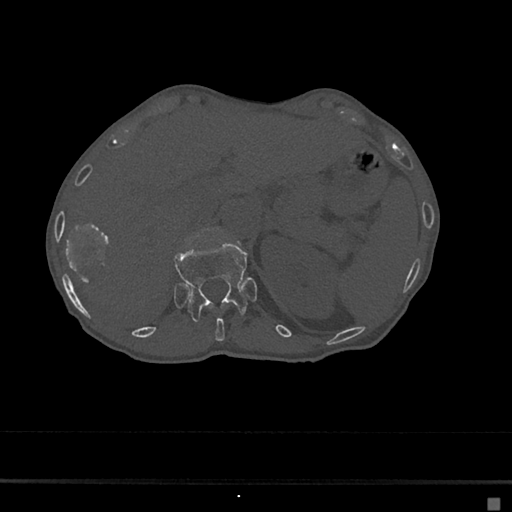
CT including the spine, one axial slice; position 132 of 797 along the scan axis; reconstruction kernel Br40s/3; 120 kVp; bone window (W 1800 / L 400 HU); 0.5 mm slice thickness; 512 × 512 image matrix, field of view 360 × 360 mm. Female patient, age 68 years. Case-level facts recorded for this patient, not image findings: primary cancer: renal.
Outlined on this slice (semi-automatic segmentation, software-assisted and operator-edited):
- T11 vertebra: bounding box (x1, y1, x2, y2) in pixels: (215, 317, 225, 342)
- T12 vertebra: (174, 242, 247, 322)